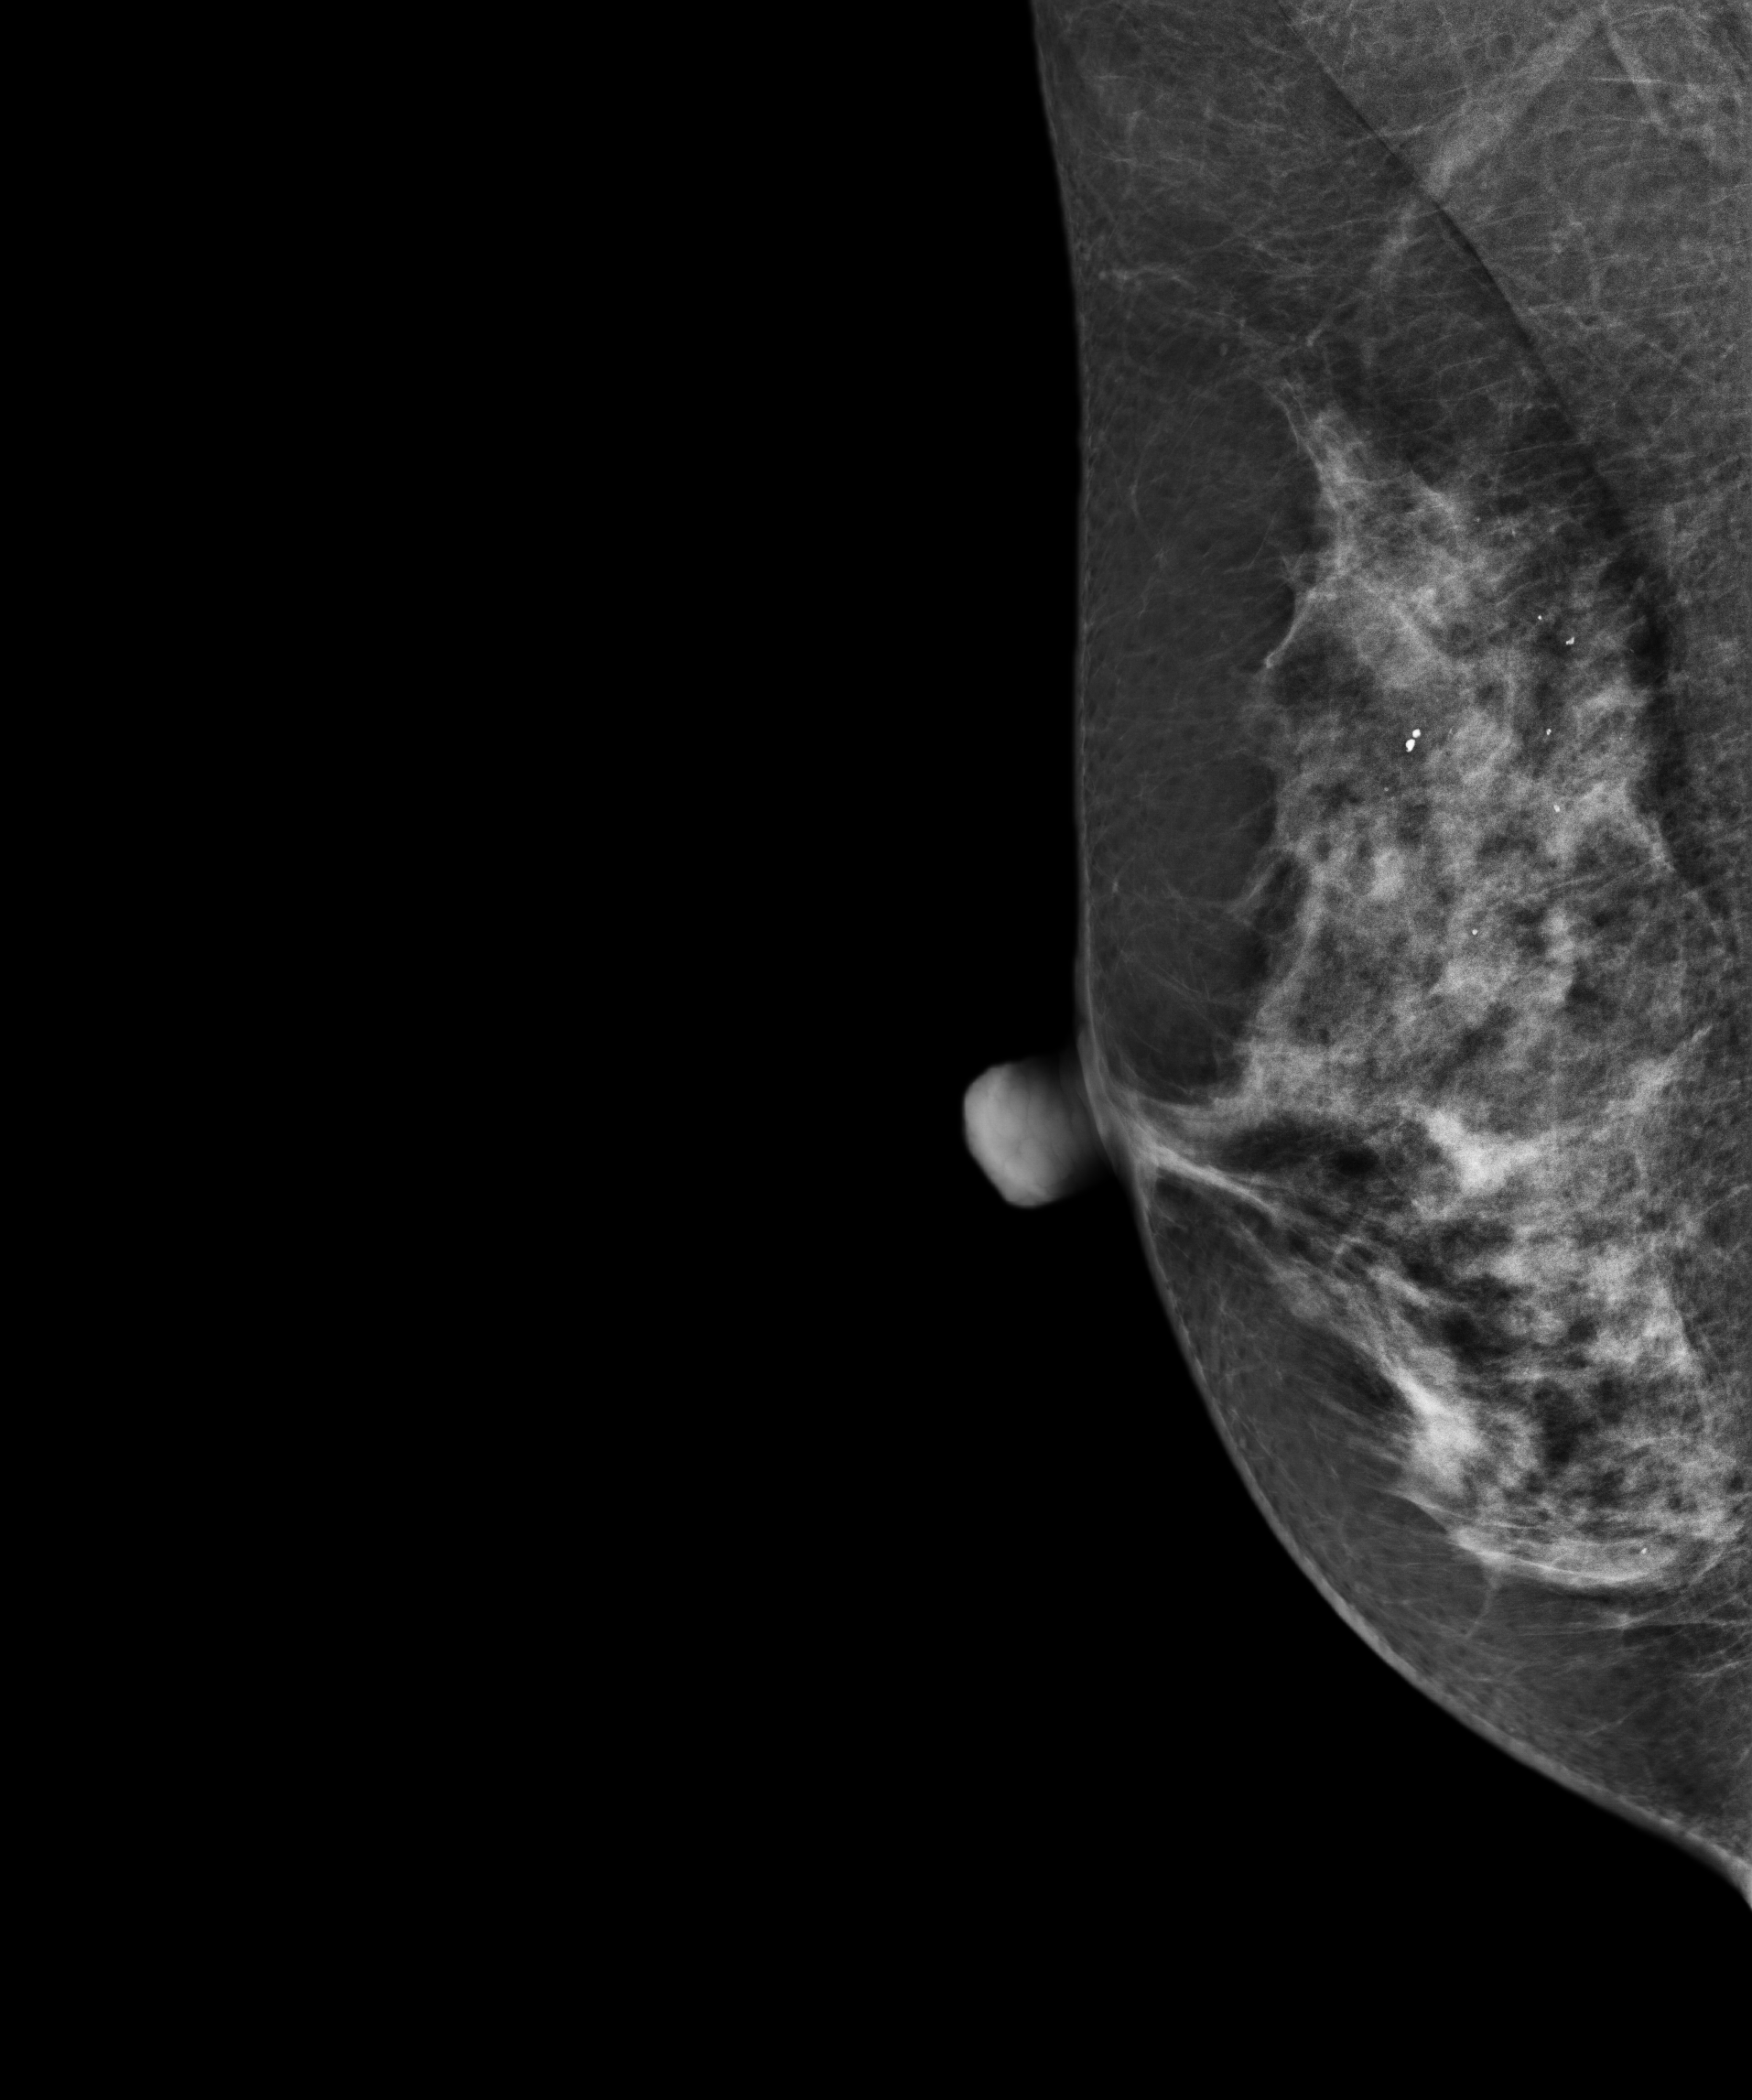
Annual screening mammography examination, system: Senographe Pristina.
Image type: full-field digital mammogram. Breast: right. Projection: MLO view.